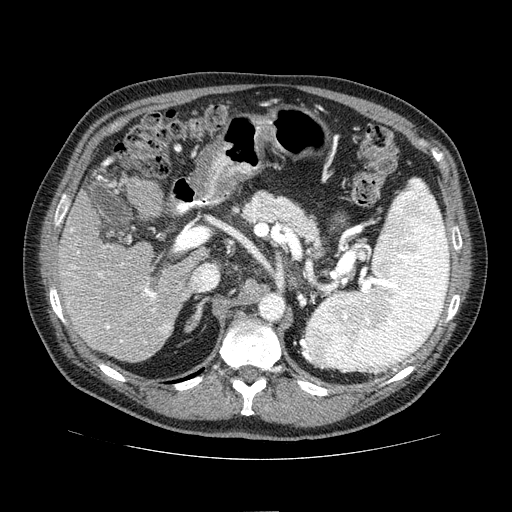
Contrast-enhanced abdominal CT (liver protocol), one axial slice; slice 39 of 81 in the series (ordered by position); one of 2 acquisitions stored at this slice position; soft-tissue window (W 400 / L 40 HU); 512 × 512 image matrix, field of view 400 × 400 mm. Case-level facts recorded for this patient, not image findings: diagnosis: hepatocellular carcinoma (patient treated with transarterial chemoembolisation; whether this scan precedes or follows treatment is not stated here); TNM stage (as recorded): Stage-IIIA; Child-Pugh class: A; tumour nodularity: multinodular.
Structures marked on this image (semi-automatic segmentation, software-assisted and operator-edited):
- liver parenchyma outside the tumour (the mass and vessels are separate outlines, so this box may not span the whole liver): box from (x=57, y=187) to (x=190, y=362) px
- liver vessels: (x=68, y=228)–(x=171, y=343)